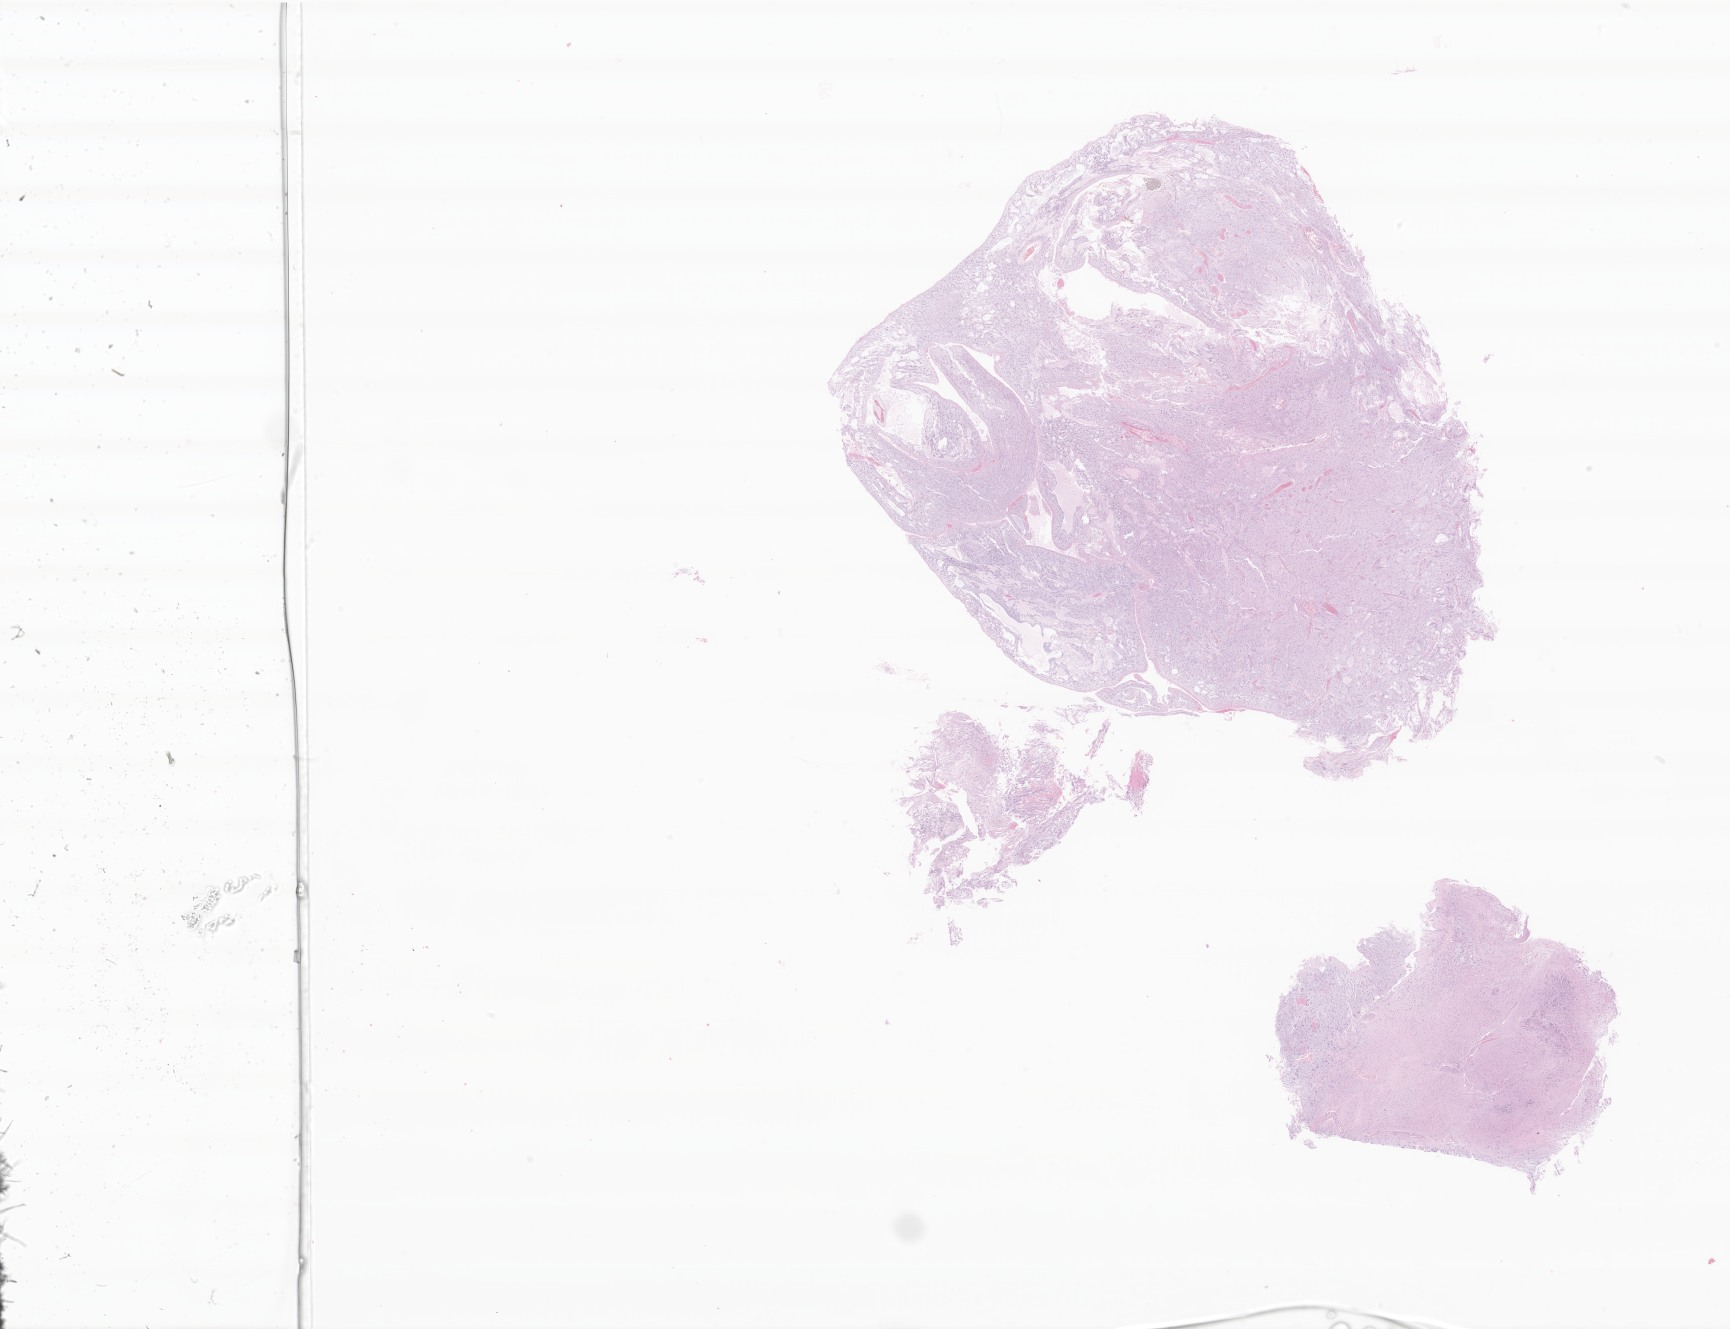
Hematoxylin and eosin (H&E) whole-slide image of tumor tissue from the brain, whole scanned area (about 29.2 x 22.4 mm) shown as a low-resolution overview. Formalin-fixed, paraffin-embedded (FFPE) tissue. Patient: female, age 168 months (14 years).
• recorded diagnosis: Pilocytic astrocytoma